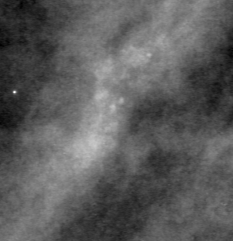
Region of interest cut from a scanned film mammogram (one marked finding), right breast, CC view, BI-RADS breast density category 3 (scale 1–4).
- Marked abnormality: calcifications, morphology pleomorphic, distribution clustered; BI-RADS assessment category 4; subtlety rating 2 on a 1 (subtle) to 5 (obvious) scale; pathology result (as recorded, not read from the image): malignant.